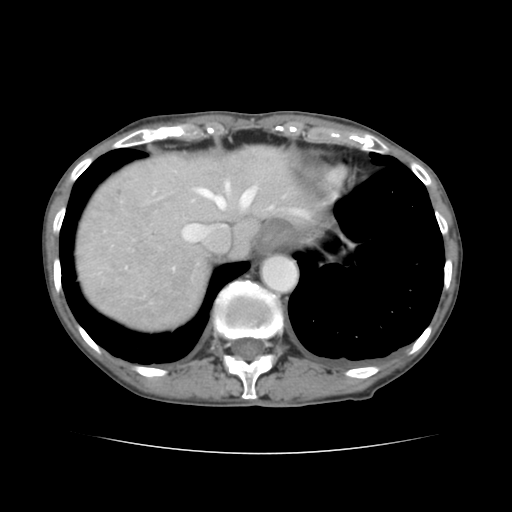
Contrast-enhanced abdominal CT, one axial slice; position 120 of 136 along the scan axis; soft-tissue window (W 400 / L 40 HU); 2.5 mm slice thickness; 512 × 512 image matrix, field of view 319 × 319 mm. Female patient, age 77 years. From the clinical record (not read from this slice): diagnosis: colorectal cancer liver metastases, imaged before liver resection; multiple liver metastases: yes; largest metastasis: 3 cm; disease in both lobes: no.
Annotated regions visible in this slice (expert manual segmentation):
- hepatic veins: bounding box [x1, y1, x2, y2] px = [181, 179, 273, 243]
- liver: [77, 147, 321, 329]
- planned liver remnant (the part of the liver to remain after resection): [177, 147, 320, 255]